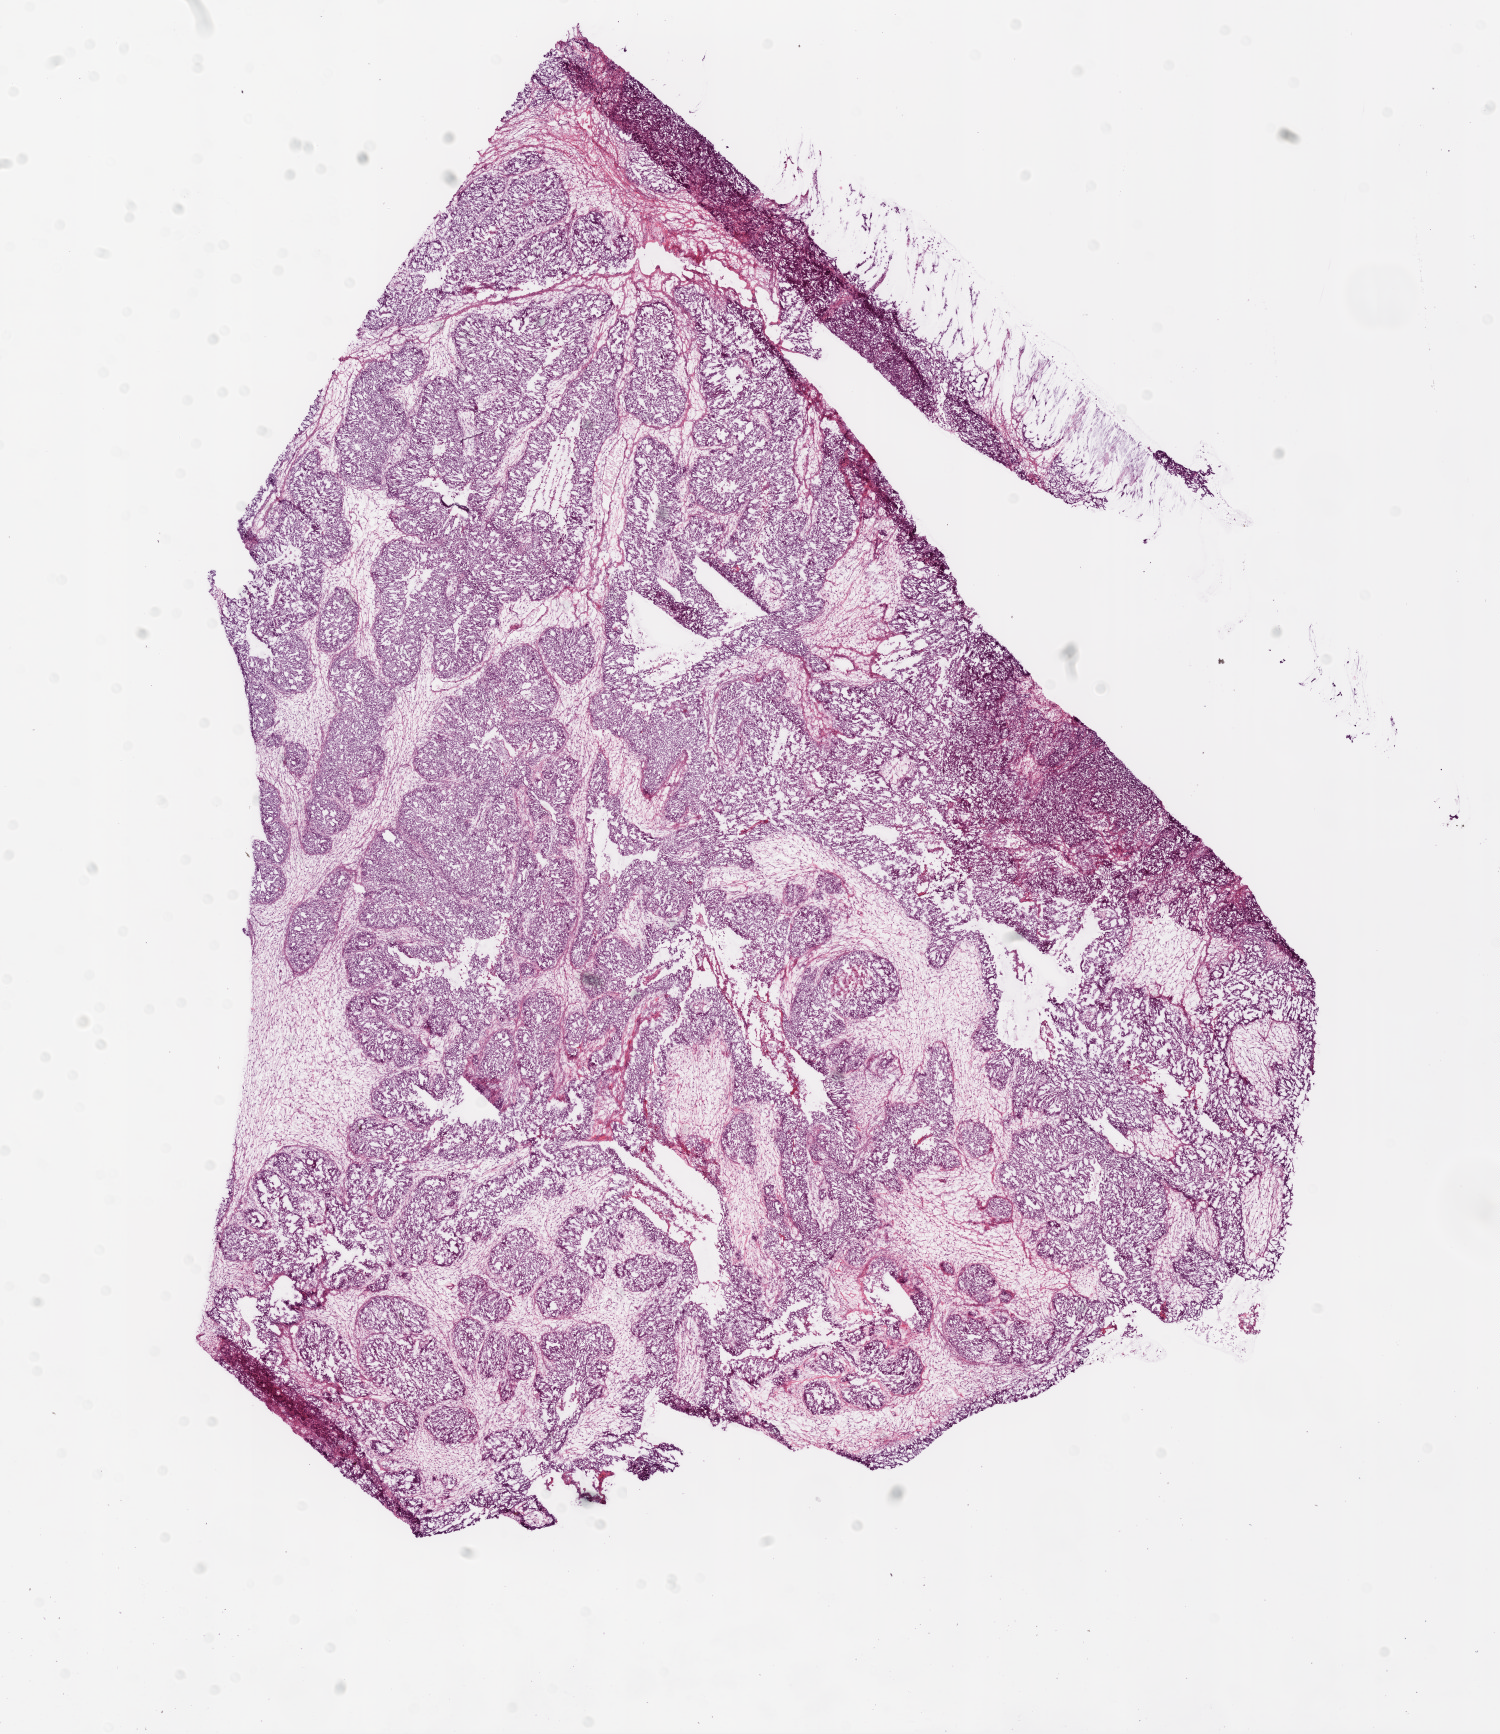
Whole-slide histology image, H&E-stained — whole scanned area (about 12.0 x 13.9 mm) shown as a low-resolution overview; frozen section from the bottom of the tissue portion; ovary, primary tumour sample. Female patient; age at initial diagnosis 54 years. Histologic grade: G3 (poorly differentiated). Slide review estimates, as recorded: tumour cells 80%, tumour nuclei 85%, normal cells 0%, stromal cells 20%, necrosis 0%. Infiltration values recorded for this section: lymphocyte infiltration 5%, monocyte infiltration 0%, neutrophil infiltration 0%.
FIGO stage: IIIA. Histologic diagnosis: Serous cystadenocarcinoma, NOS.